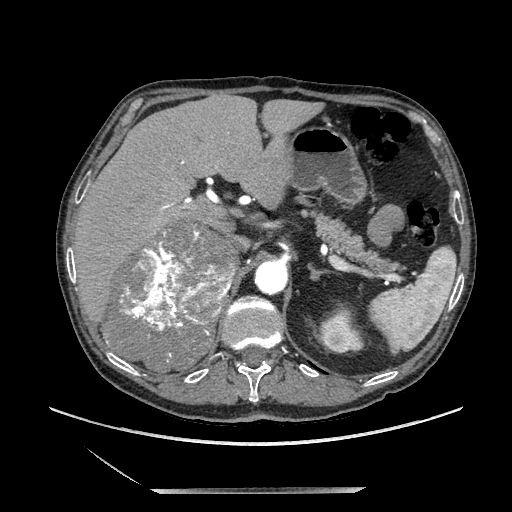
Contrast-enhanced abdominal CT, one axial slice. Position 142 of 243 along the scan axis. Soft-tissue window (W 400 / L 40 HU). 1.25 mm slice thickness. 512 × 512 image matrix. Male patient. From the clinical record (not read from this slice): diagnosis: adrenocortical carcinoma; tumour side: right adrenal; tumour size at pathology: 16 cm; Ki-67 index: 17 %; stage (as recorded): 3.
Annotated regions visible in this slice (semi-automatic segmentation, software-assisted and operator-edited):
- mass: bounding box [x1, y1, x2, y2] px = [103, 222, 232, 369]